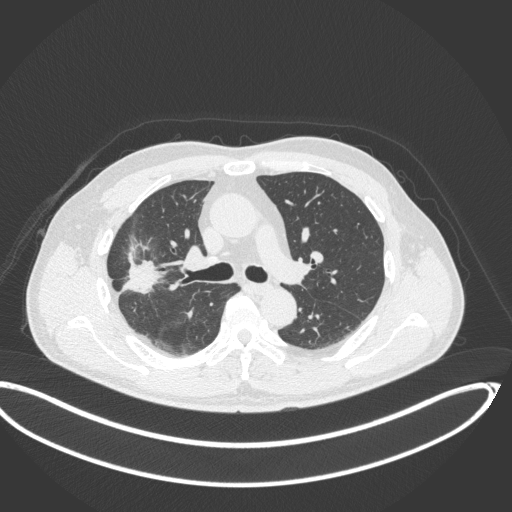
Chest CT, one axial slice. Position 216 of 341 along the scan axis. Reconstruction kernel B31f. 120 kVp. Lung window (W 1500 / L -600 HU). 512 × 512 image matrix, field of view 439 × 439 mm. Patient: male, 63 years. Case-level facts recorded for this patient, not image findings: clinical TNM (as recorded): T1c N0 M0.
Annotated regions visible in this slice (rectangle marked by the reading radiologist):
- lung tumour (recorded histology: adenocarcinoma): bounding box <118,254,161,299> (left, top, right, bottom; pixels)